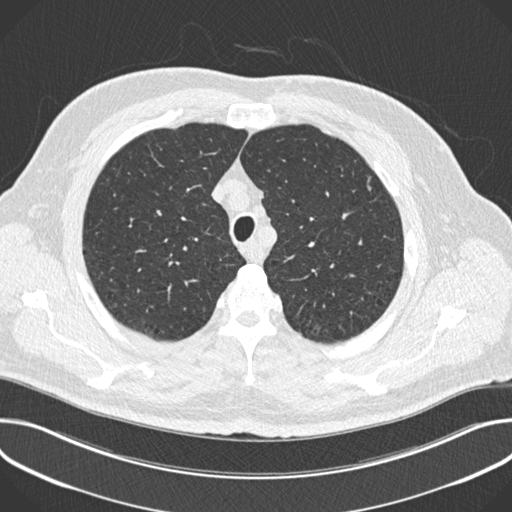
Axial slice from a low-dose chest CT screening exam. Baseline annual screen. Lung window (W 1500 / L -600 HU). Male, age 63 years at enrolment. Current smoker at enrolment.
Expert-annotated lung lesion, bounding box (x1, y1, x2, y2) in pixels: (358, 166, 385, 201). The screening reader recorded 2 non-calcified nodules or masses ≥4 mm on this exam; which of them this box marks is not recorded. Official screen result: positive, change unspecified: nodule(s) >= 4 mm or enlarging nodule(s), mass(es), or other non-specific abnormalities suspicious for lung cancer.